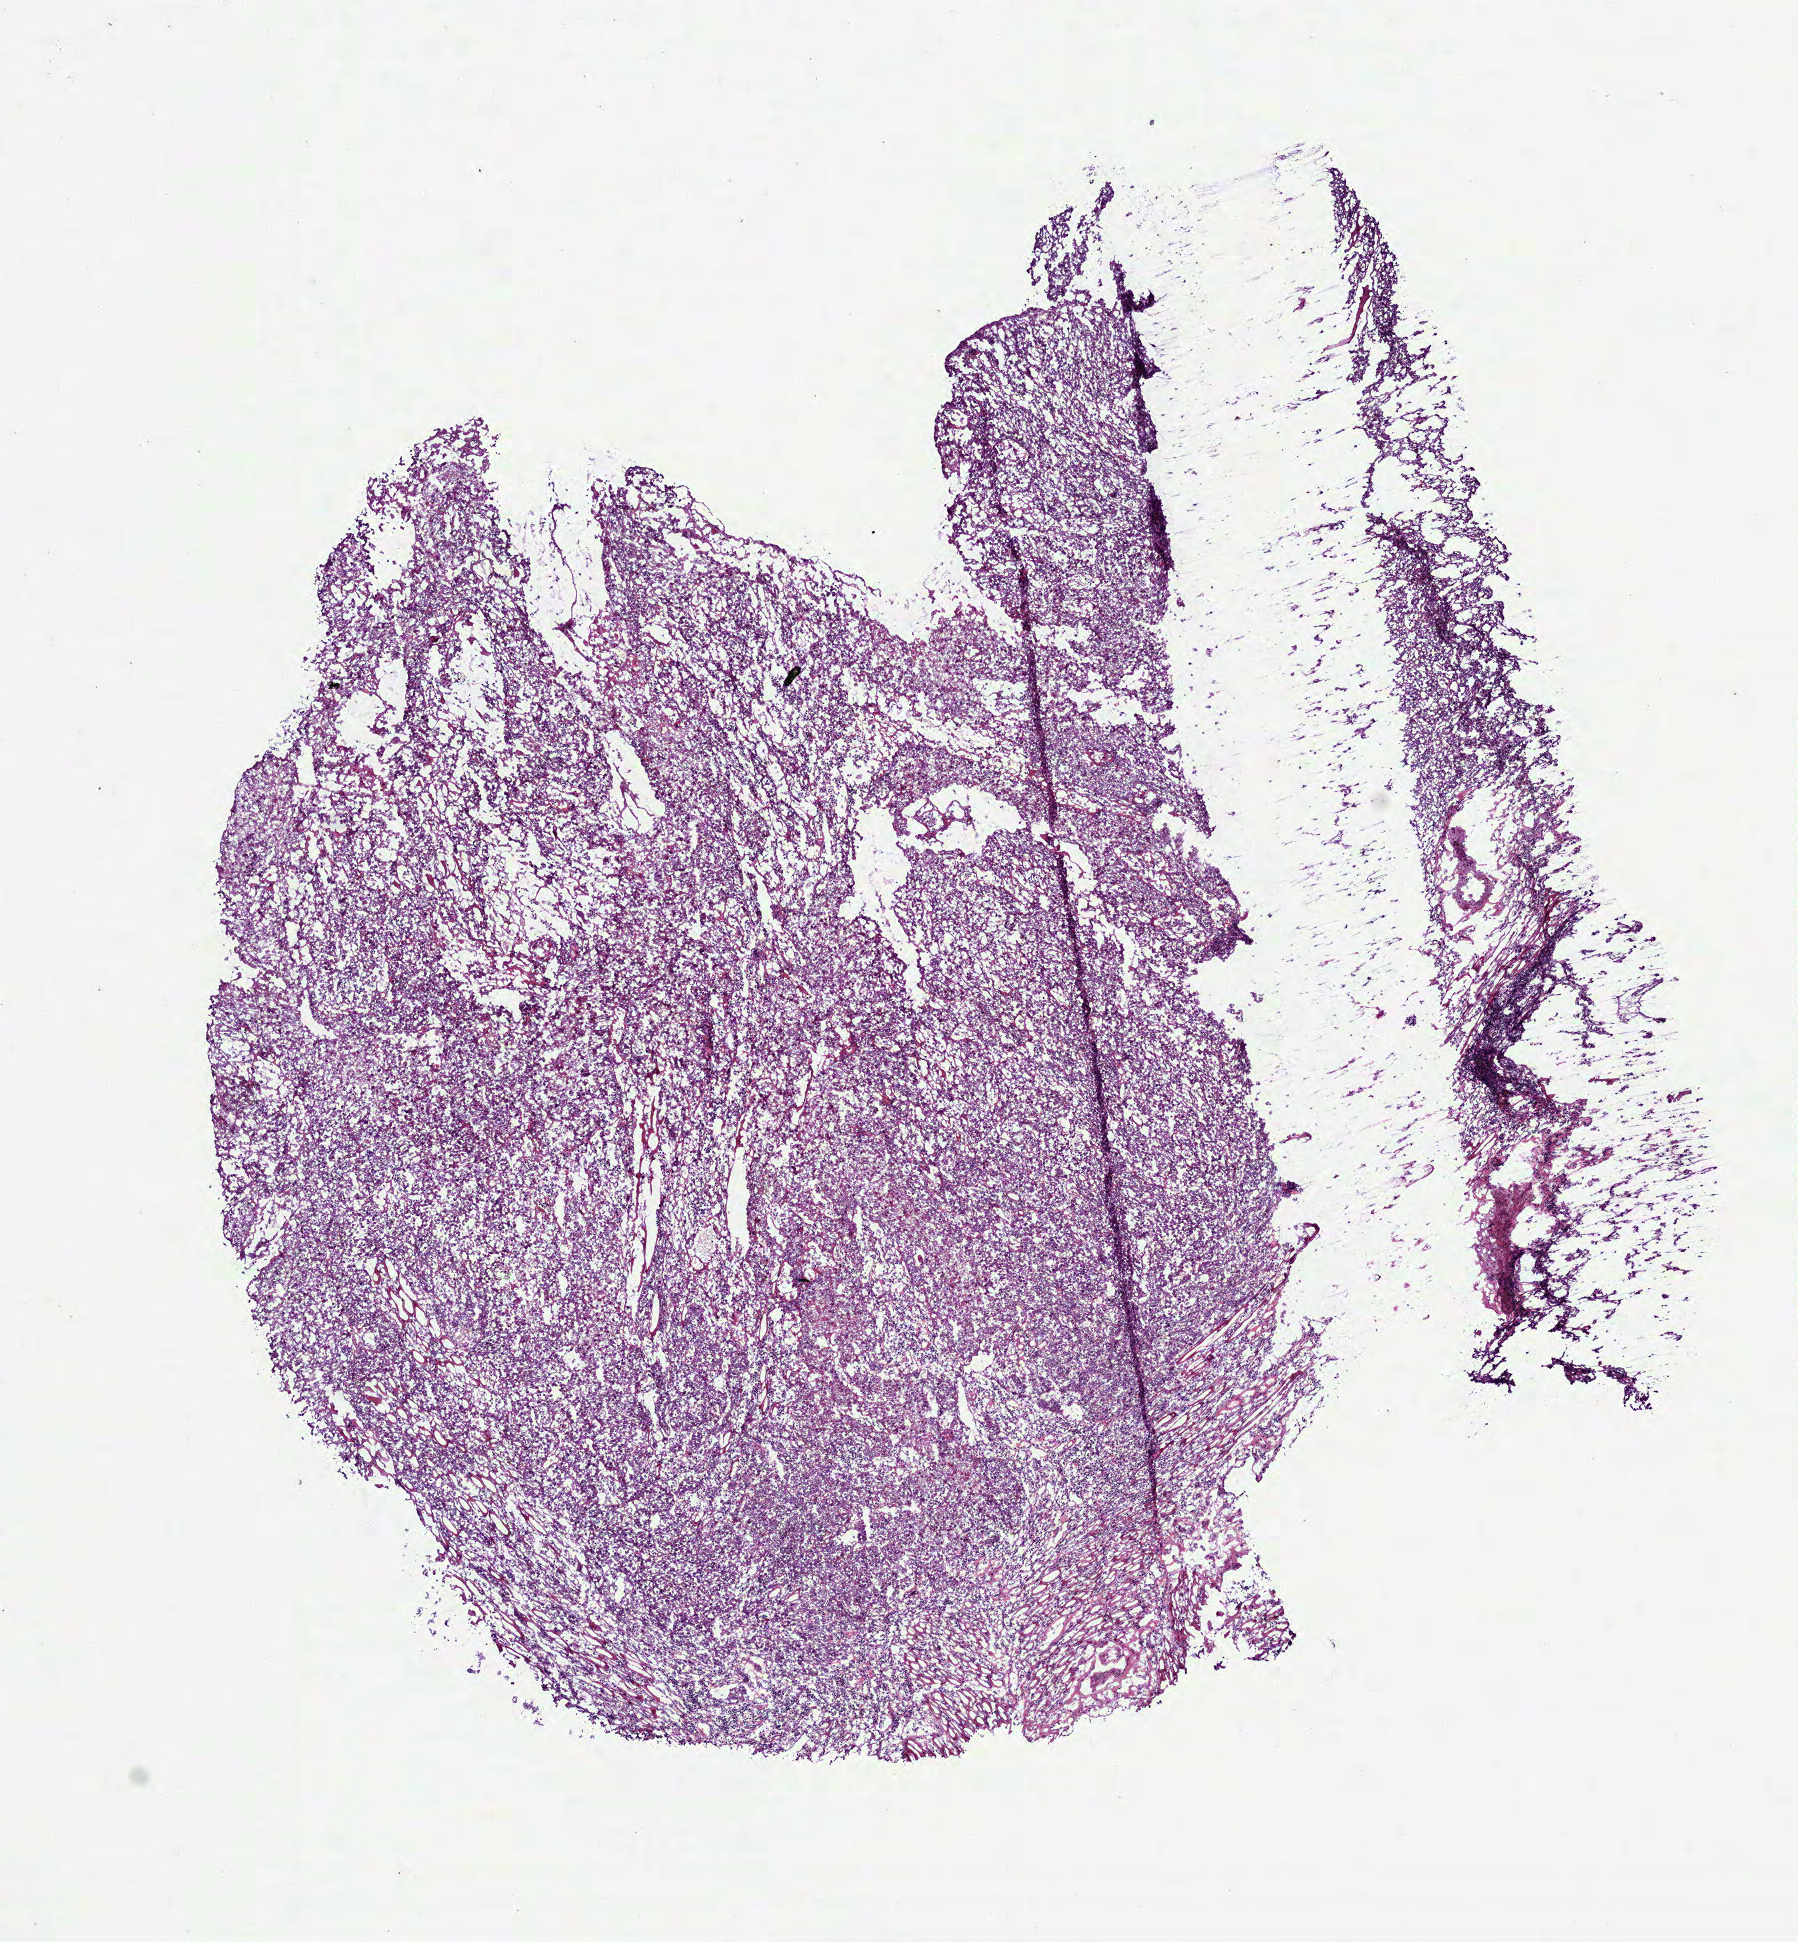
H&E-stained whole-slide image, shown as a low-resolution overview of the whole scanned area (about 7.3 x 7.8 mm). Frozen section from the bottom of the tissue portion. Head and neck, primary tumour sample. Male, age 55 years at initial diagnosis. Histologic grade: G2 (moderately differentiated). Pathologist review of this section (percent, as recorded): tumour cells 85%, tumour nuclei 80%, normal cells 0%, stromal cells 10%, necrosis 5%.
Diagnosis: Squamous cell carcinoma, NOS (tongue, NOS). AJCC pathologic stage: IVA (7th edition). TNM: T3 N2b.